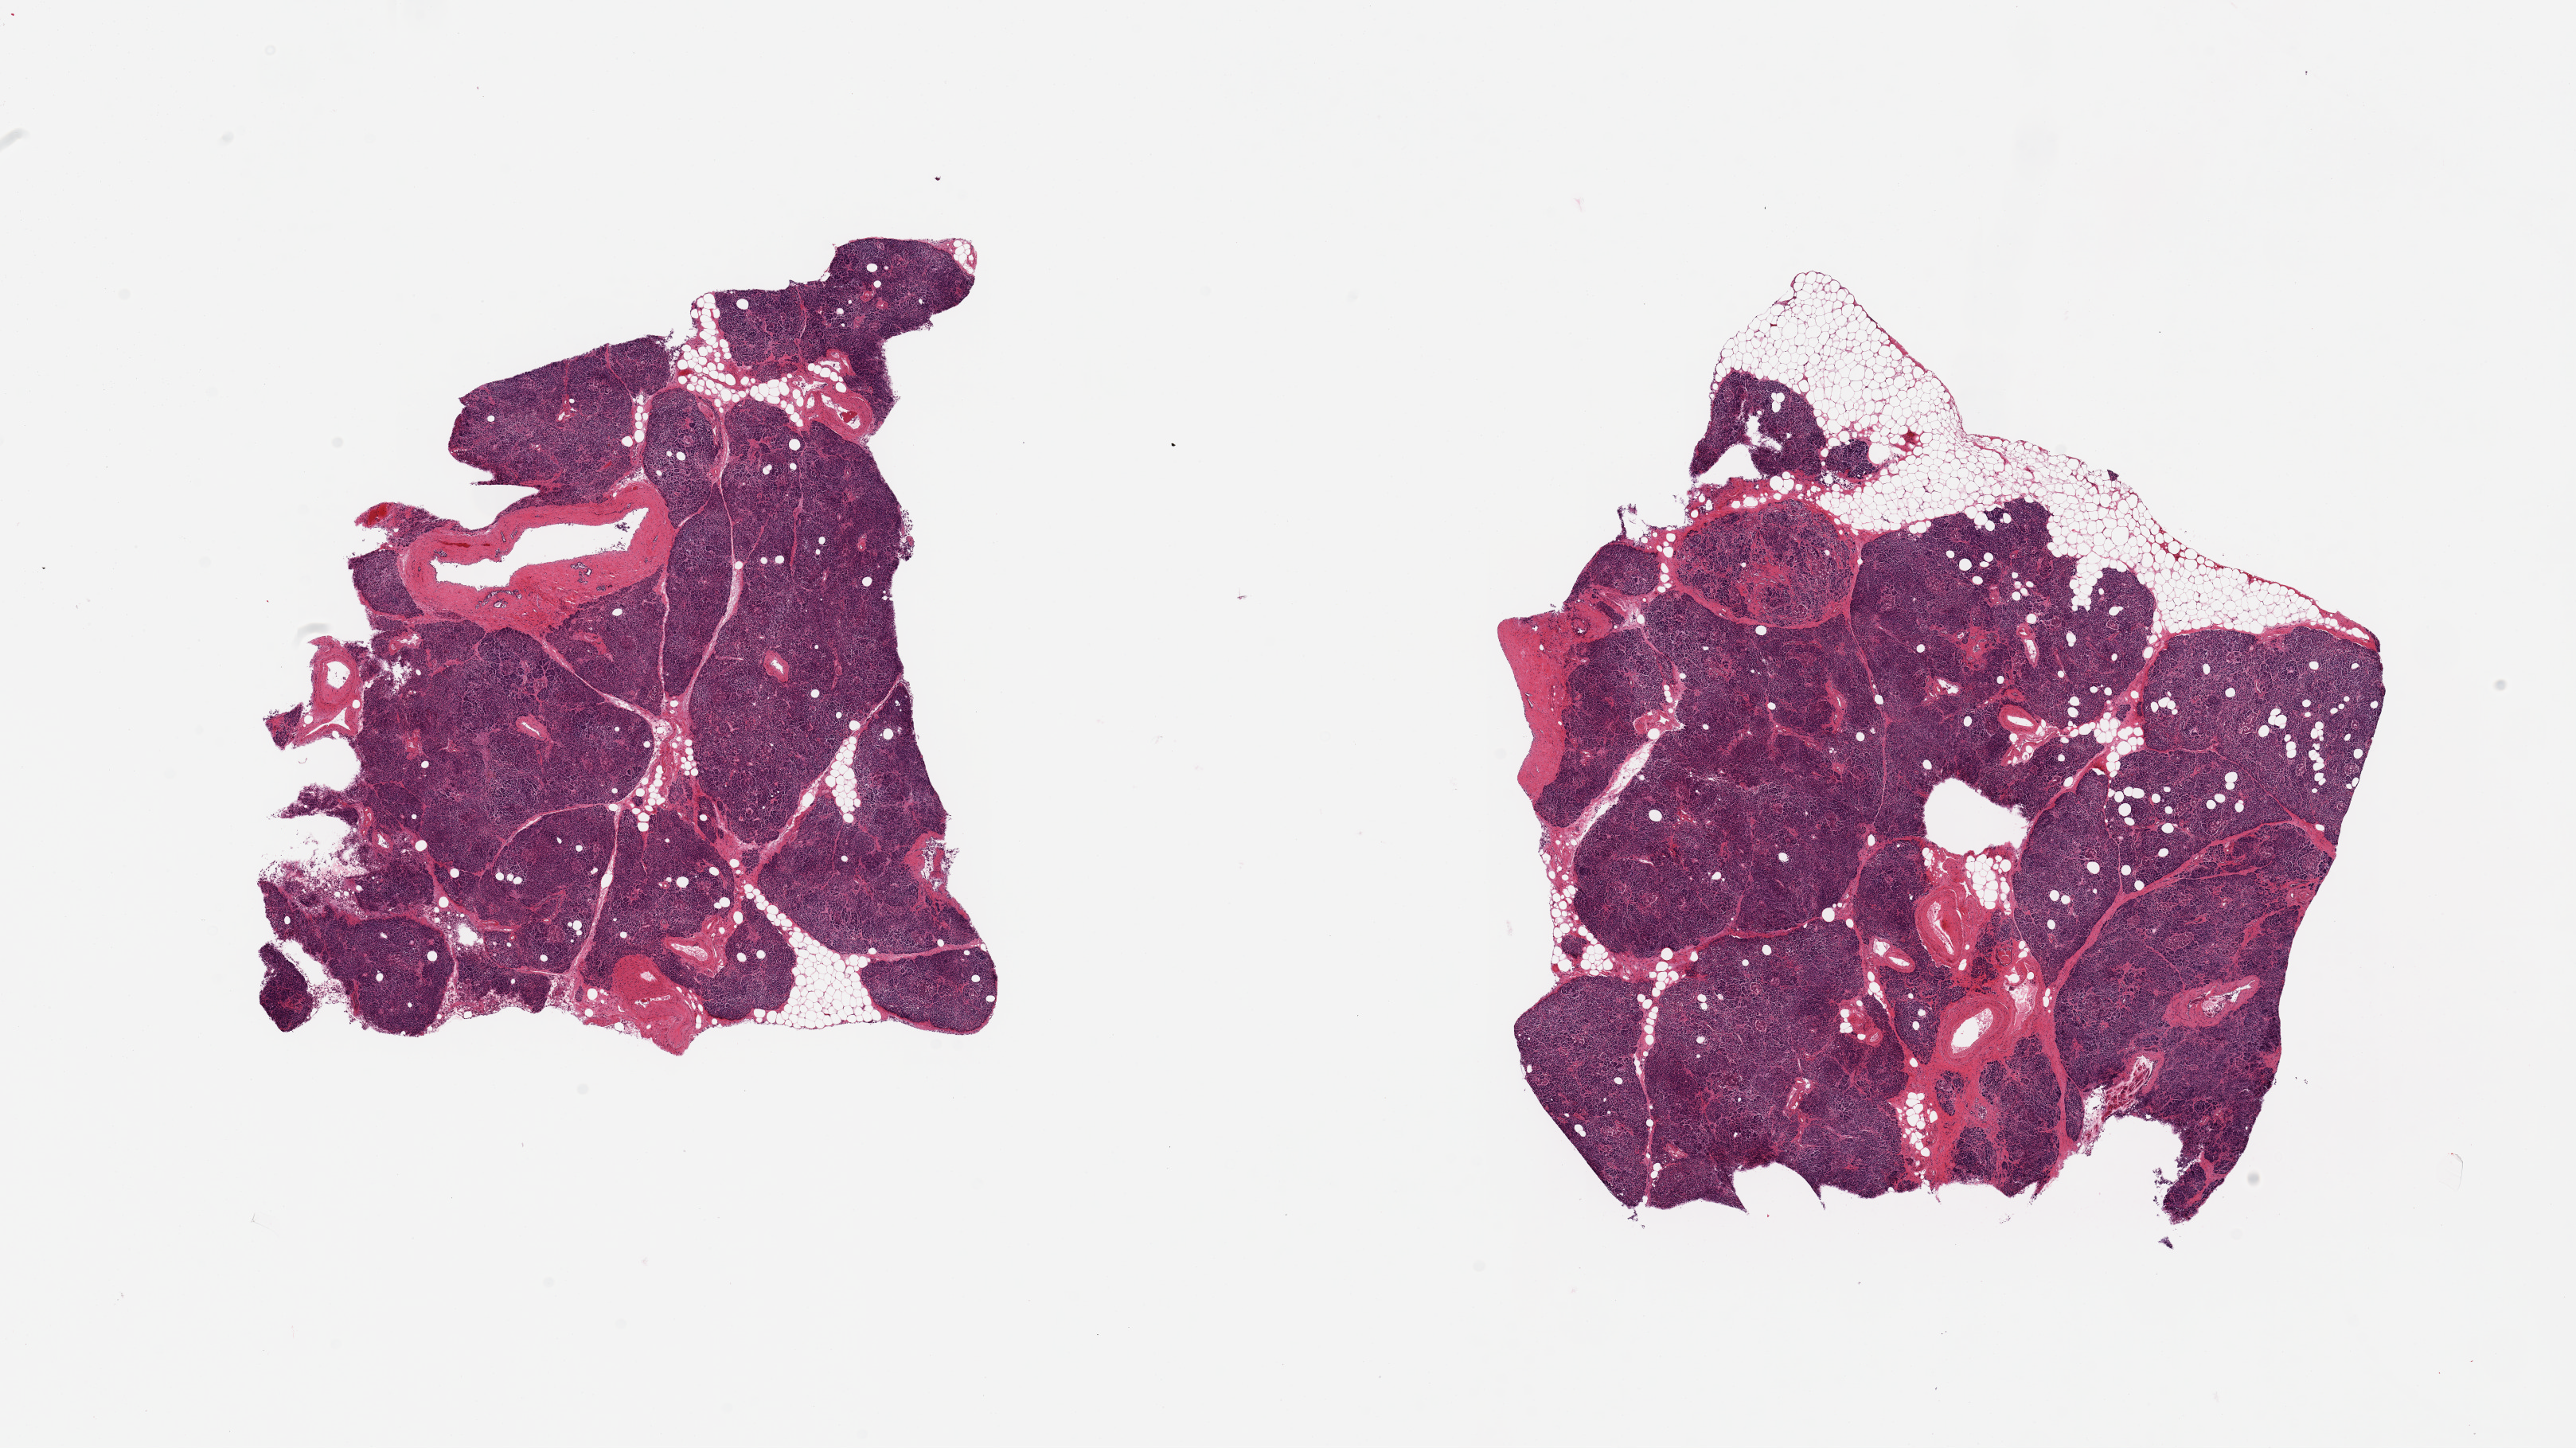
Hematoxylin and eosin (H&E) whole-slide image, a low-resolution overview of the entire scanned area, about 25.6 x 14.4 mm; PAXgene-fixed, paraffin-embedded tissue; sampled site (target tissue): pancreas; tissue donor sample. Donor: male.
Pathologist's review note for this sample: 2 pieces; one contains 10% of external fat and other with minimal amount of fat.